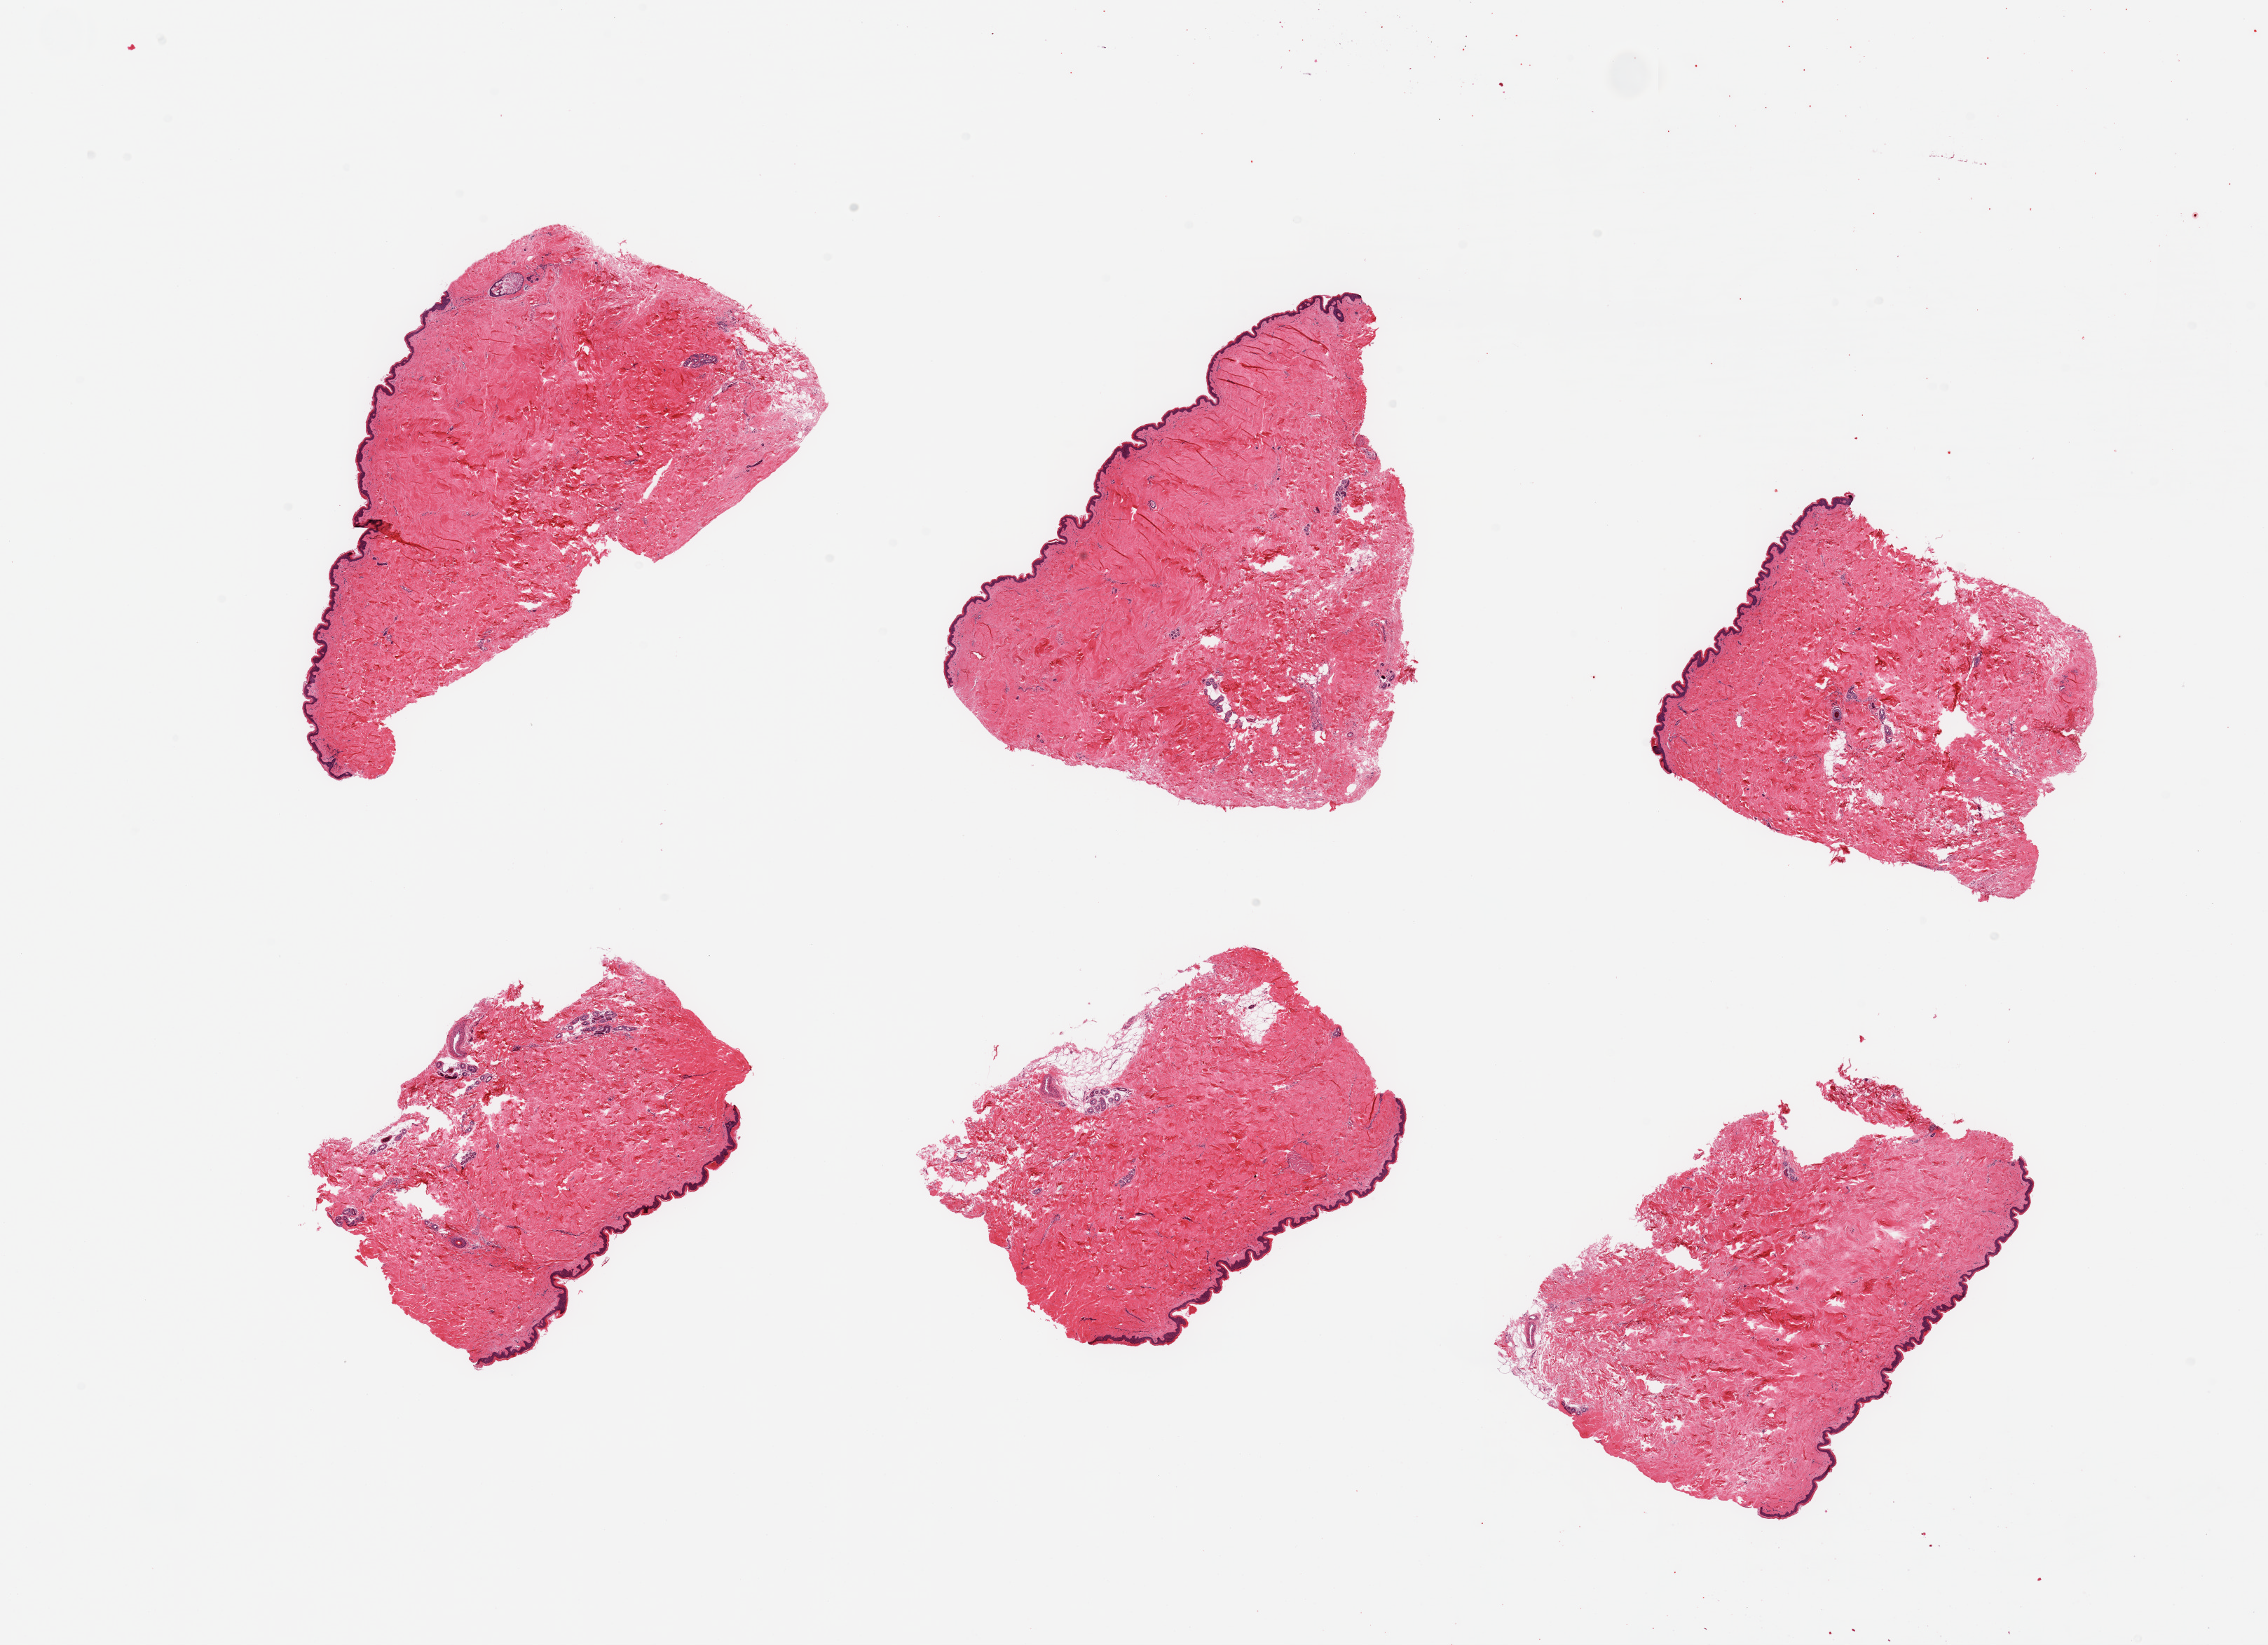
Whole-slide image, haematoxylin and eosin stain, whole scanned area (about 25.6 x 18.6 mm) shown as a low-resolution overview, PAXgene-fixed, paraffin-embedded tissue, sampled site (target tissue): skin of suprapubic region, donor tissue sample. Donor sex: female.
Reviewer comment on this tissue sample: 6 pieces, no dermal fat; squamous epithelium is ~20-50 microns.